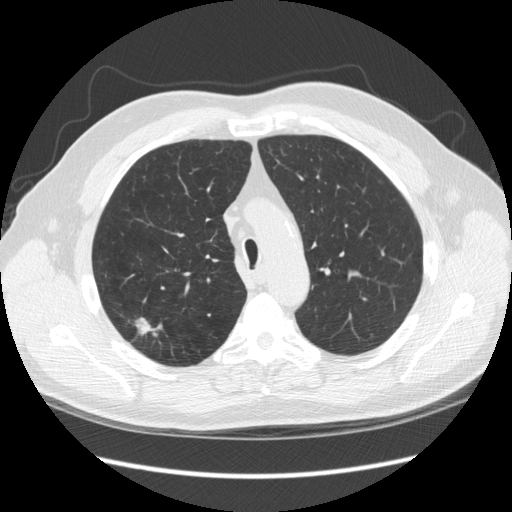
Chest CT (low-dose screening protocol), one axial image, third screening round (two years after baseline), lung window (W 1500 / L -600 HU), 2.5 mm slice thickness, standard (soft-tissue) reconstruction kernel (STANDARD), slice 65 of 248 in the series, 512 × 512 image matrix. Male, age 64 years at enrolment. Former smoker at enrolment.
- Expert reader's lesion annotation, bounding box [x1, y1, x2, y2] px = [117, 314, 169, 357].
- The screening reader recorded 4 non-calcified nodules or masses ≥4 mm on this exam; which of them this box marks is not recorded.
- Participant outcome: lung cancer diagnosed 15 days after this screen — adenocarcinoma, NOS, right upper lobe, moderately differentiated (G2), stage IA (AJCC 6th edition), 14 mm at pathology.